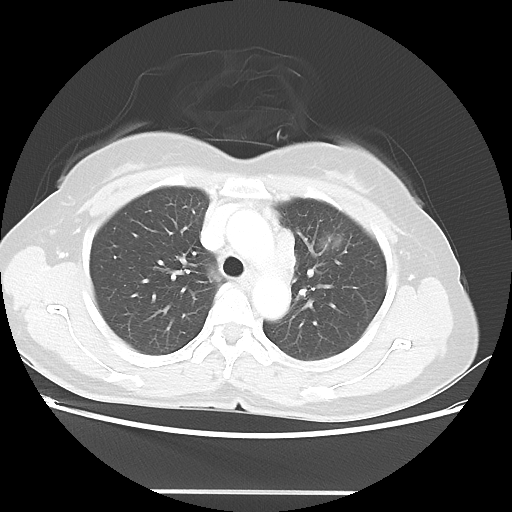
Chest CT, one axial slice. Slice 33 of 46 in the series (ordered by position). Reconstruction kernel LUNG. 100 kVp. Lung window (W 1500 / L -600 HU). 512 × 512 image matrix. Patient: female, 50 years. Case-level facts recorded for this patient, not image findings: clinical TNM (as recorded): T1c N1 M0; histopathological grade: G3.
Annotated regions visible in this slice (bounding box drawn by a radiologist):
- lung tumour (recorded histology: adenocarcinoma): bounding box (x1, y1, x2, y2) in pixels: (317, 231, 346, 253)